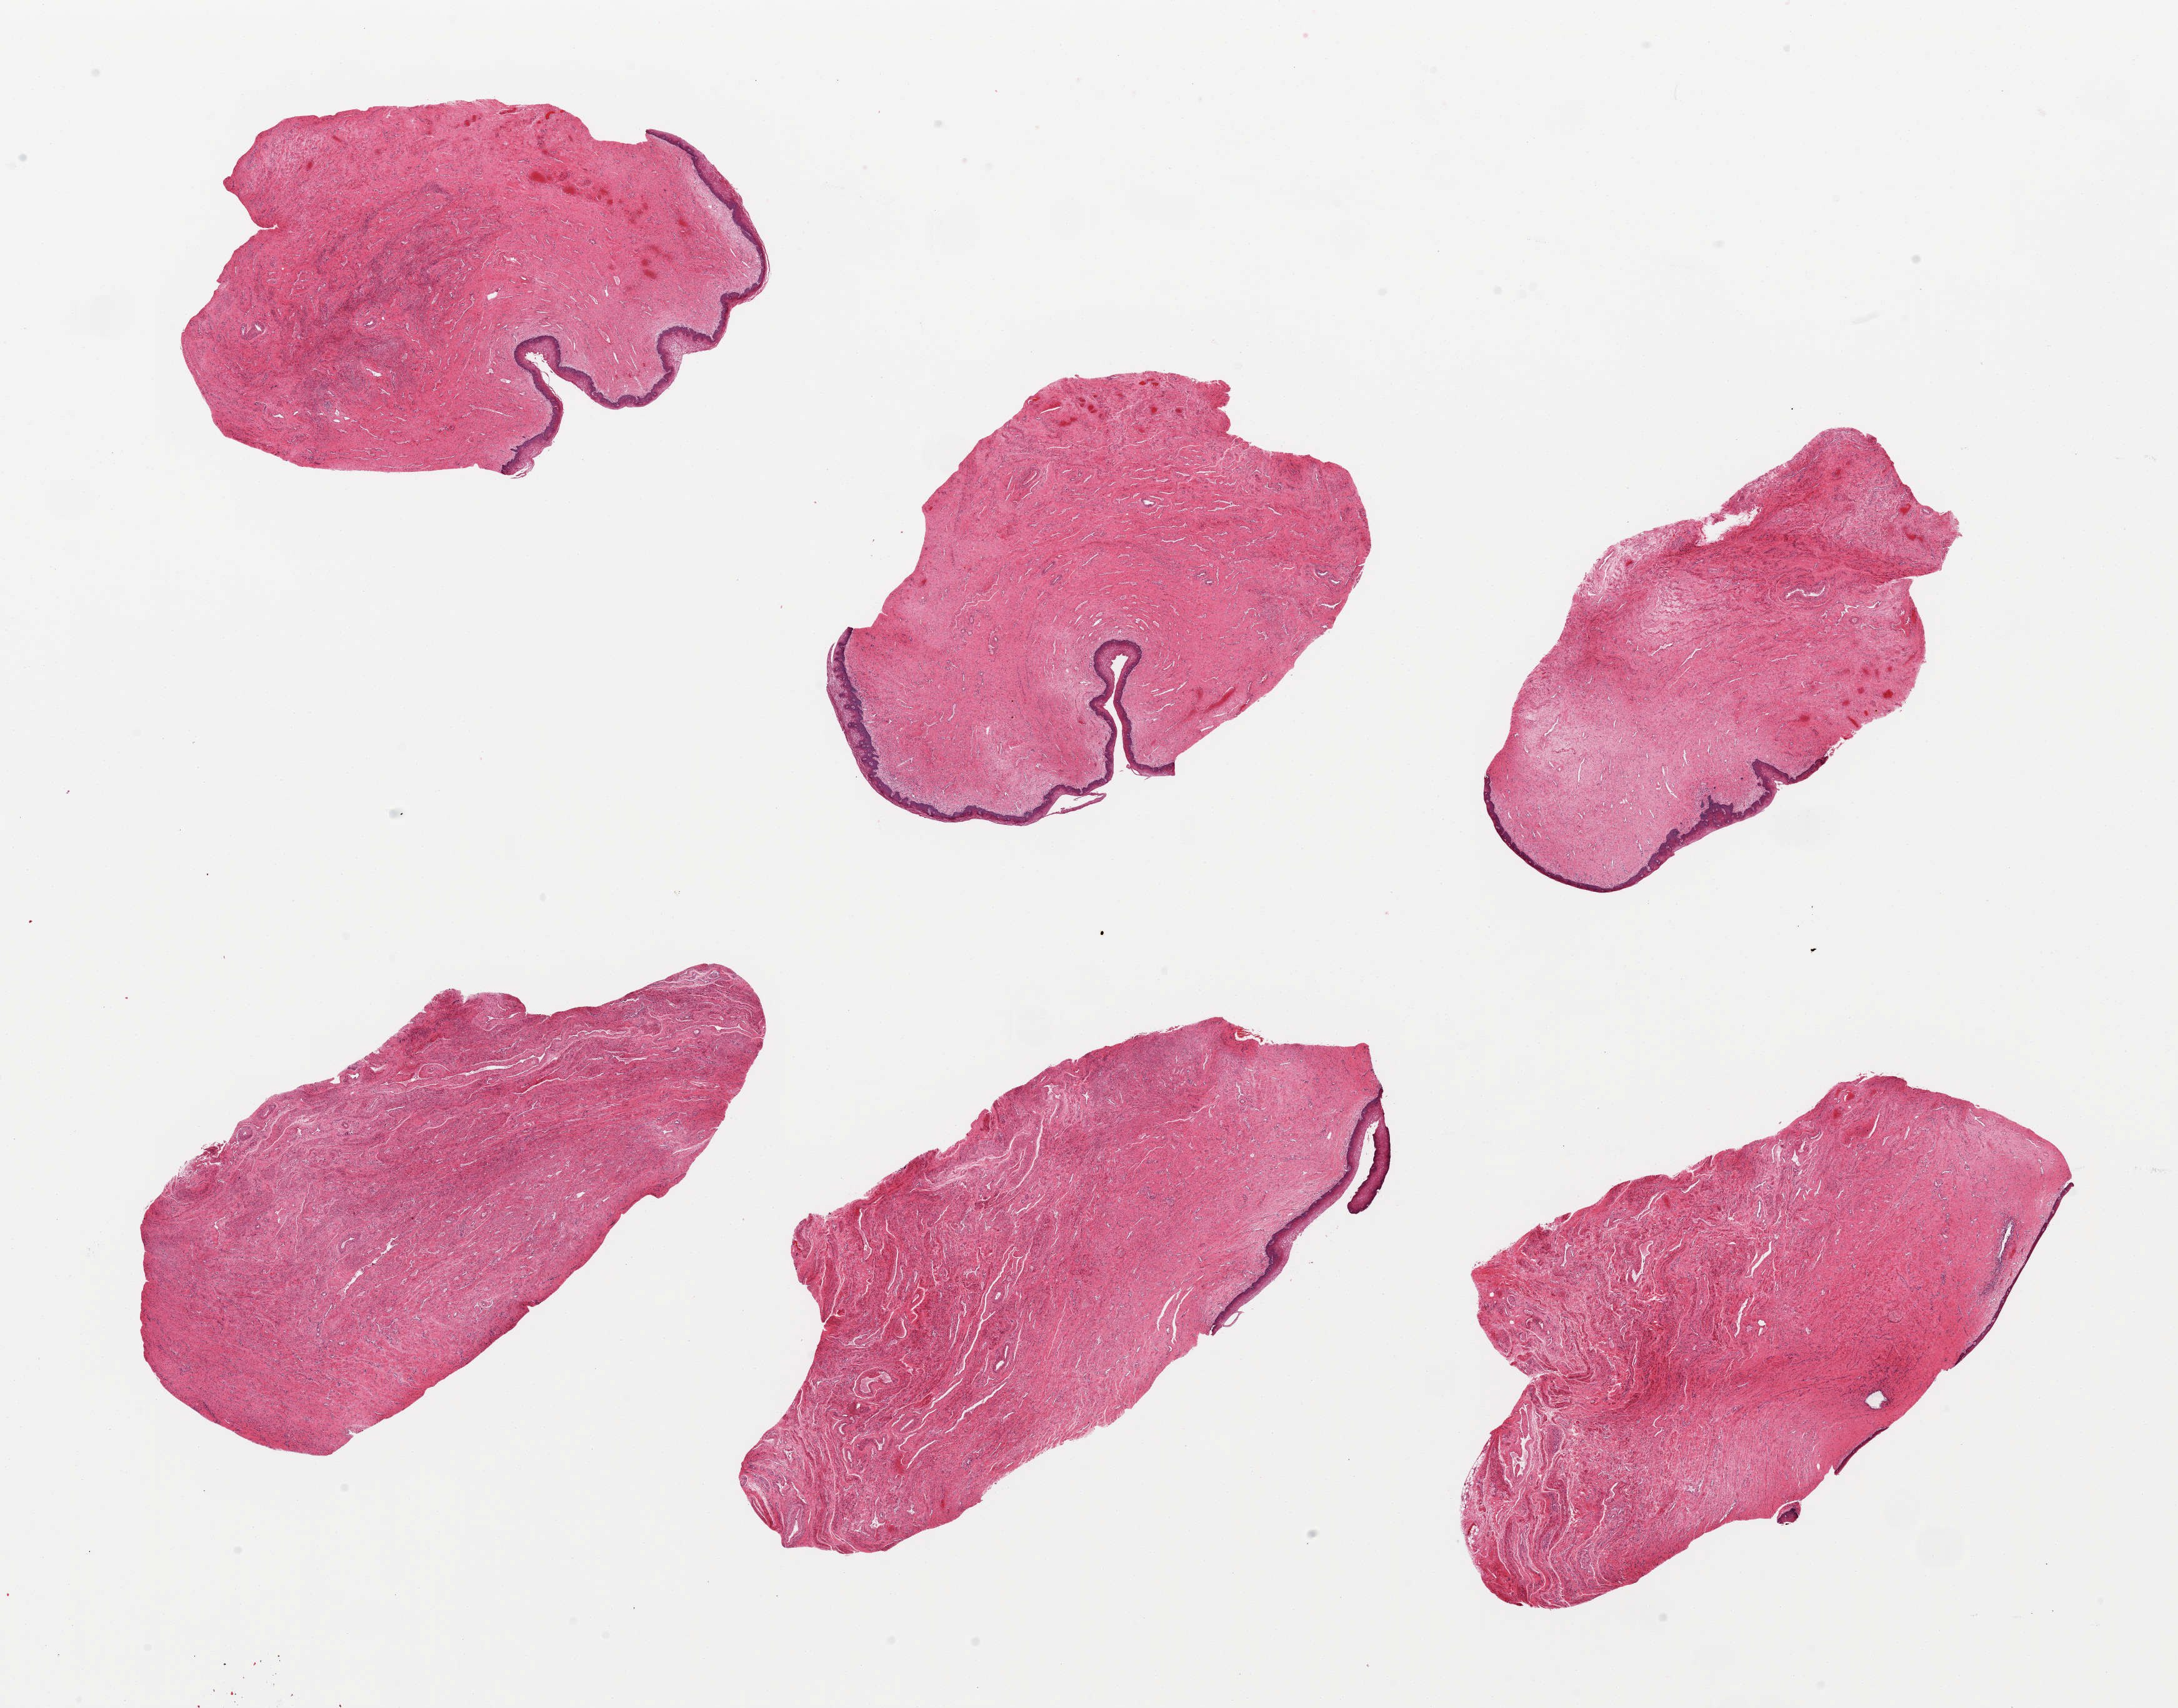
Digitized hematoxylin and eosin (H&E)-stained section — shown as a low-resolution overview of the whole scanned area (about 27.6 x 21.6 mm, from a 20x scan). PAXgene-fixed, paraffin-embedded tissue. Target tissue: vagina. Donor tissue sample.
Reviewer comment on this tissue sample: 6 pieces; epithelium partially sloughed.